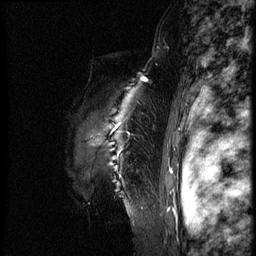
Breast MRI (dynamic contrast-enhanced), one sagittal slice. Slice 58 of 66 in the series (ordered by position). Dynamic contrast-enhanced series, image 2 of 3 at this slice position (ordered by acquisition). 1.5 T. TE 4.2 ms, TR 8.9 ms. 256 × 256 image matrix, field of view 200 × 200 mm. Female patient, age 39 years. Case-level facts recorded for this patient, not image findings: setting: breast cancer imaged before/during neoadjuvant chemotherapy; receptor status: HER2-positive.
Outlined on this slice (semi-automatically segmented with operator editing):
- analysis volume of interest (the breast-tissue region the enhancement analysis was run in; not a lesion): bounding box [x1, y1, x2, y2] px = [65, 75, 161, 218]
- tumour enhancement mask (voxels above the 140 % enhancement threshold inside the analysis volume of interest): [143, 79, 147, 82]